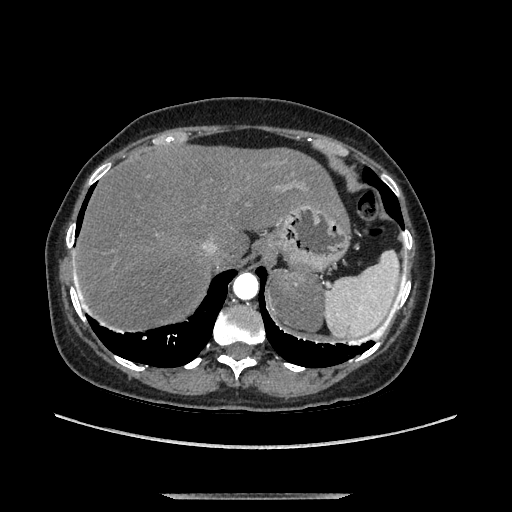
Contrast-enhanced abdominal CT, one axial slice. Slice 112 of 169 in the series (ordered by position). Soft-tissue window (W 400 / L 40 HU). 1.25 mm slice thickness. 512 × 512 image matrix, field of view 400 × 400 mm. Female patient. Case-level facts recorded for this patient, not image findings: diagnosis: adrenocortical carcinoma; tumour side: left adrenal; tumour size at pathology: 9 cm; Ki-67 index: 2 %; stage (as recorded): 3.
Outlined on this slice (semi-automatically segmented with operator editing):
- mass: box from (x=274, y=275) to (x=322, y=328) px